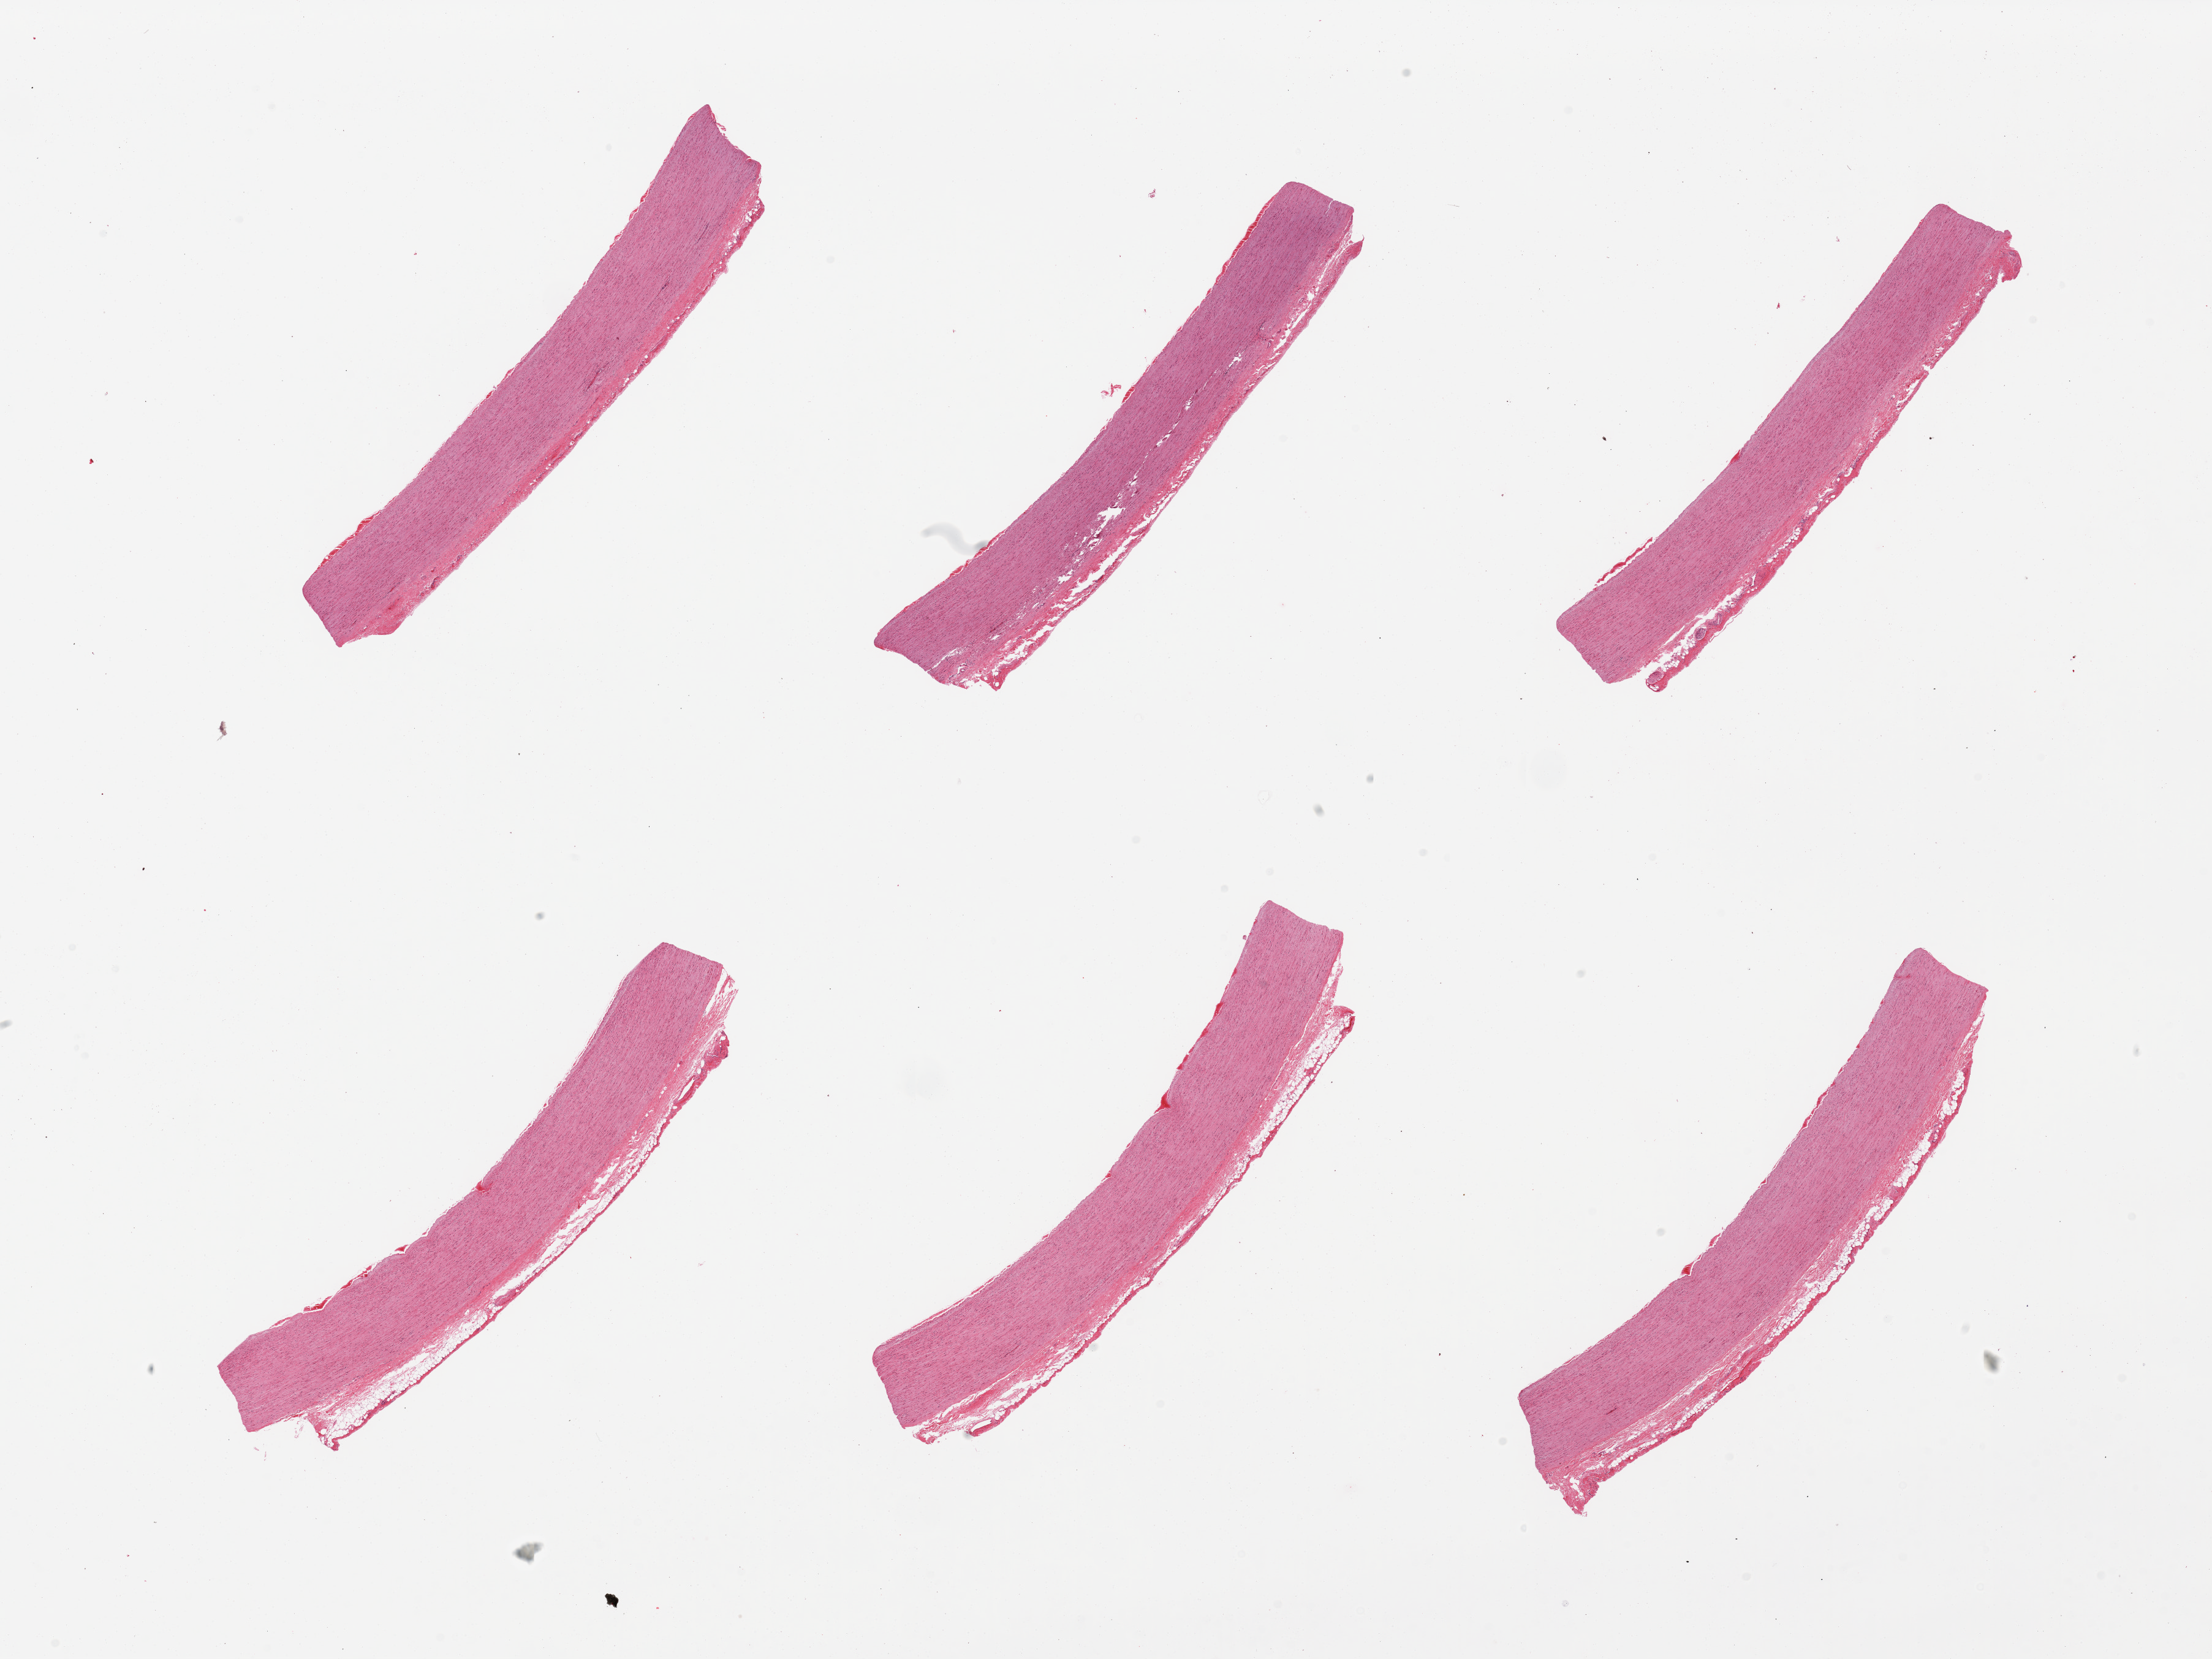
Whole-slide image, H&E stain — low-resolution overview of the scanned area, about 28.5 x 21.4 mm. PAXgene-fixed, paraffin-embedded tissue. Sampled site (target tissue): aorta. Tissue donor sample. Donor sex: male.
Reviewer comment on this tissue sample: 6 pieces, minimal atherosis/adherent serosa.